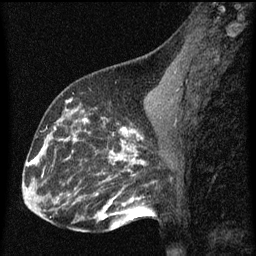
Breast MRI (dynamic contrast-enhanced), one sagittal slice. Position 29 of 60 along the scan axis. Dynamic contrast-enhanced series, image 2 of 3 at this slice position (ordered by acquisition). 1.5 T. TE 4.2 ms, TR 8 ms. 2 mm slice thickness. 256 × 256 image matrix, field of view 180 × 180 mm. Female patient, age 43 years.
Outlined on this slice (semi-automatically segmented with operator editing):
- analysis volume of interest (the breast-tissue region the enhancement analysis was run in; not a lesion): bounding box [x1, y1, x2, y2] px = [53, 104, 101, 155]
- tumour enhancement mask (voxels above the 70 % enhancement threshold inside the analysis volume of interest): [54, 104, 91, 141]